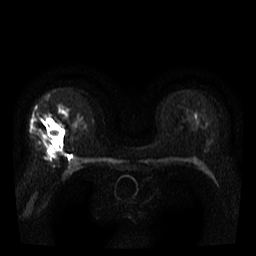
Breast MRI, one axial slice; position 23 of 40 along the scan axis; diffusion-weighted series; image 2 of 4 stored at this slice position (different b-values; order by instance number); 3 T; 5 mm slice thickness; 256 × 256 image matrix, field of view 300 × 300 mm. Female patient.
Outlined on this slice (outlined manually by an expert reader):
- tumour on diffusion-weighted imaging: bounding box [x1, y1, x2, y2] px = [49, 124, 64, 141]